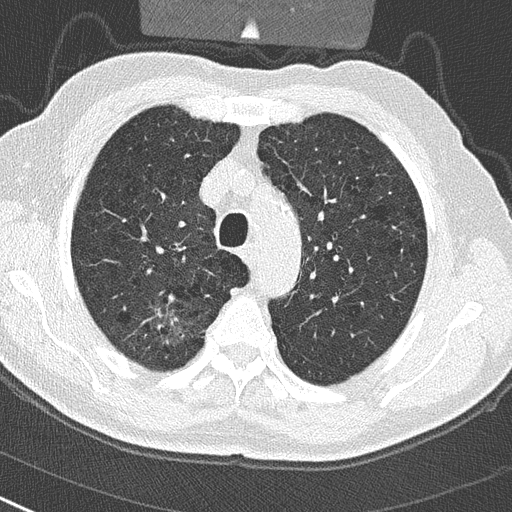
Axial slice from a low-dose chest CT screening exam; baseline screening round; lung window (W 1500 / L -600 HU); 120 kVp; slice 71 of 290 in the series. Male participant, aged 65 years at enrolment. Current smoker at enrolment.
Expert-annotated lung lesion, bounding box [x1, y1, x2, y2] px = [129, 298, 199, 361]. Reader record for this screening exam (exam-level; its link to the box is not recorded): non-calcified nodule or mass ≥4 mm, right upper lobe, 24 × 19 mm, spiculated (stellate) margins, soft tissue attenuation. Official screen result: positive, change unspecified: nodule(s) >= 4 mm or enlarging nodule(s), mass(es), or other non-specific abnormalities suspicious for lung cancer. Lung cancer was diagnosed 32 days after this screen: non-small cell carcinoma, right upper lobe, poorly differentiated (G3), stage IA (AJCC 6th edition), 29 mm at pathology.